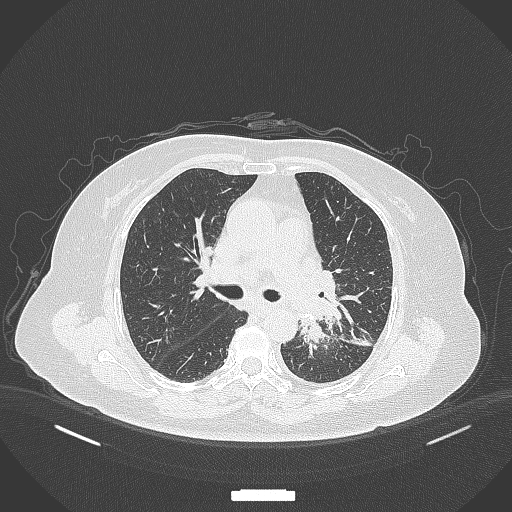
Chest CT, one axial slice; position 216 of 322 along the scan axis; 120 kVp; lung window (W 1500 / L -600 HU); 1 mm slice thickness; 512 × 512 image matrix. Female patient, age 69 years. Case-level facts recorded for this patient, not image findings: clinical TNM (as recorded): T2b N3 M1.
Structures marked on this image (bounding box drawn by a radiologist):
- lung tumour (recorded histology: adenocarcinoma): box from (x=294, y=314) to (x=331, y=353) px